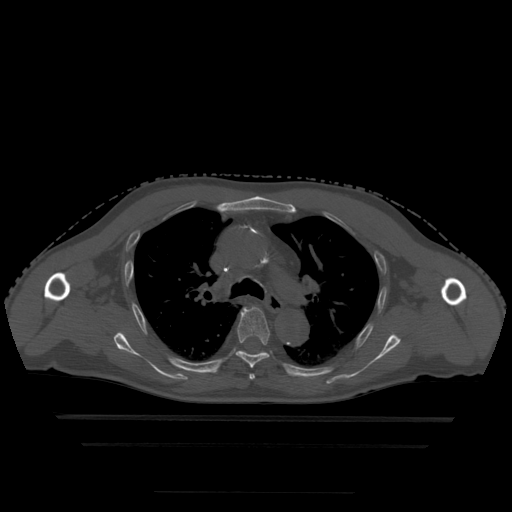
CT including the spine, one axial slice. Bone window (W 1800 / L 400 HU). 1.25 mm slice thickness. 512 × 512 image matrix, field of view 436 × 436 mm. Patient age 68 years. From the clinical record (not read from this slice): primary cancer: urothelial.
Structures marked on this image (semi-automatic segmentation, software-assisted and operator-edited):
- T4 vertebra: bounding box [x1, y1, x2, y2] px = [250, 375, 255, 380]
- T5 vertebra: [236, 308, 270, 369]